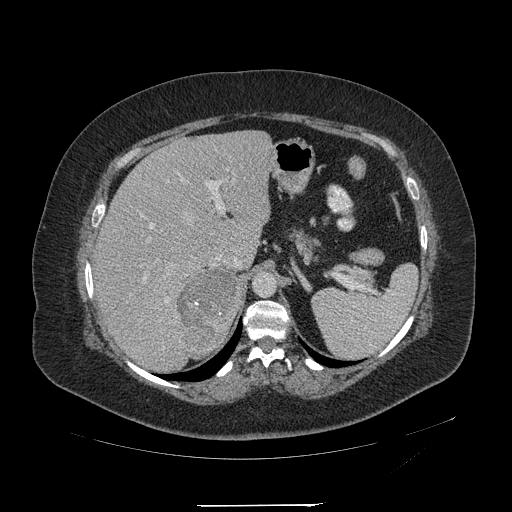
Contrast-enhanced abdominal CT, one axial slice. Slice 149 of 217 in the series (ordered by position). Reconstruction kernel STANDARD. 120 kVp. Intravenous contrast given. Soft-tissue window (W 400 / L 40 HU). 1.25 mm slice thickness. 512 × 512 image matrix, field of view 453 × 453 mm. Patient: female, 55 years. Case-level facts recorded for this patient, not image findings: diagnosis: adrenocortical carcinoma; tumour side: right adrenal.
Outlined on this slice (semi-automatic segmentation, software-assisted and operator-edited):
- mass: bounding box [x1, y1, x2, y2] px = [179, 269, 240, 353]